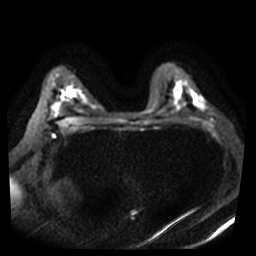
Breast MRI, one axial slice. Position 29 of 40 along the scan axis. Diffusion-weighted series; image 2 of 4 stored at this slice position (different b-values; order by instance number). 3 T. 5 mm slice thickness. 256 × 256 image matrix, field of view 360 × 360 mm. Female patient.
Outlined on this slice (expert manual segmentation):
- tumour on diffusion-weighted imaging: bounding box [x1, y1, x2, y2] px = [198, 103, 201, 106]